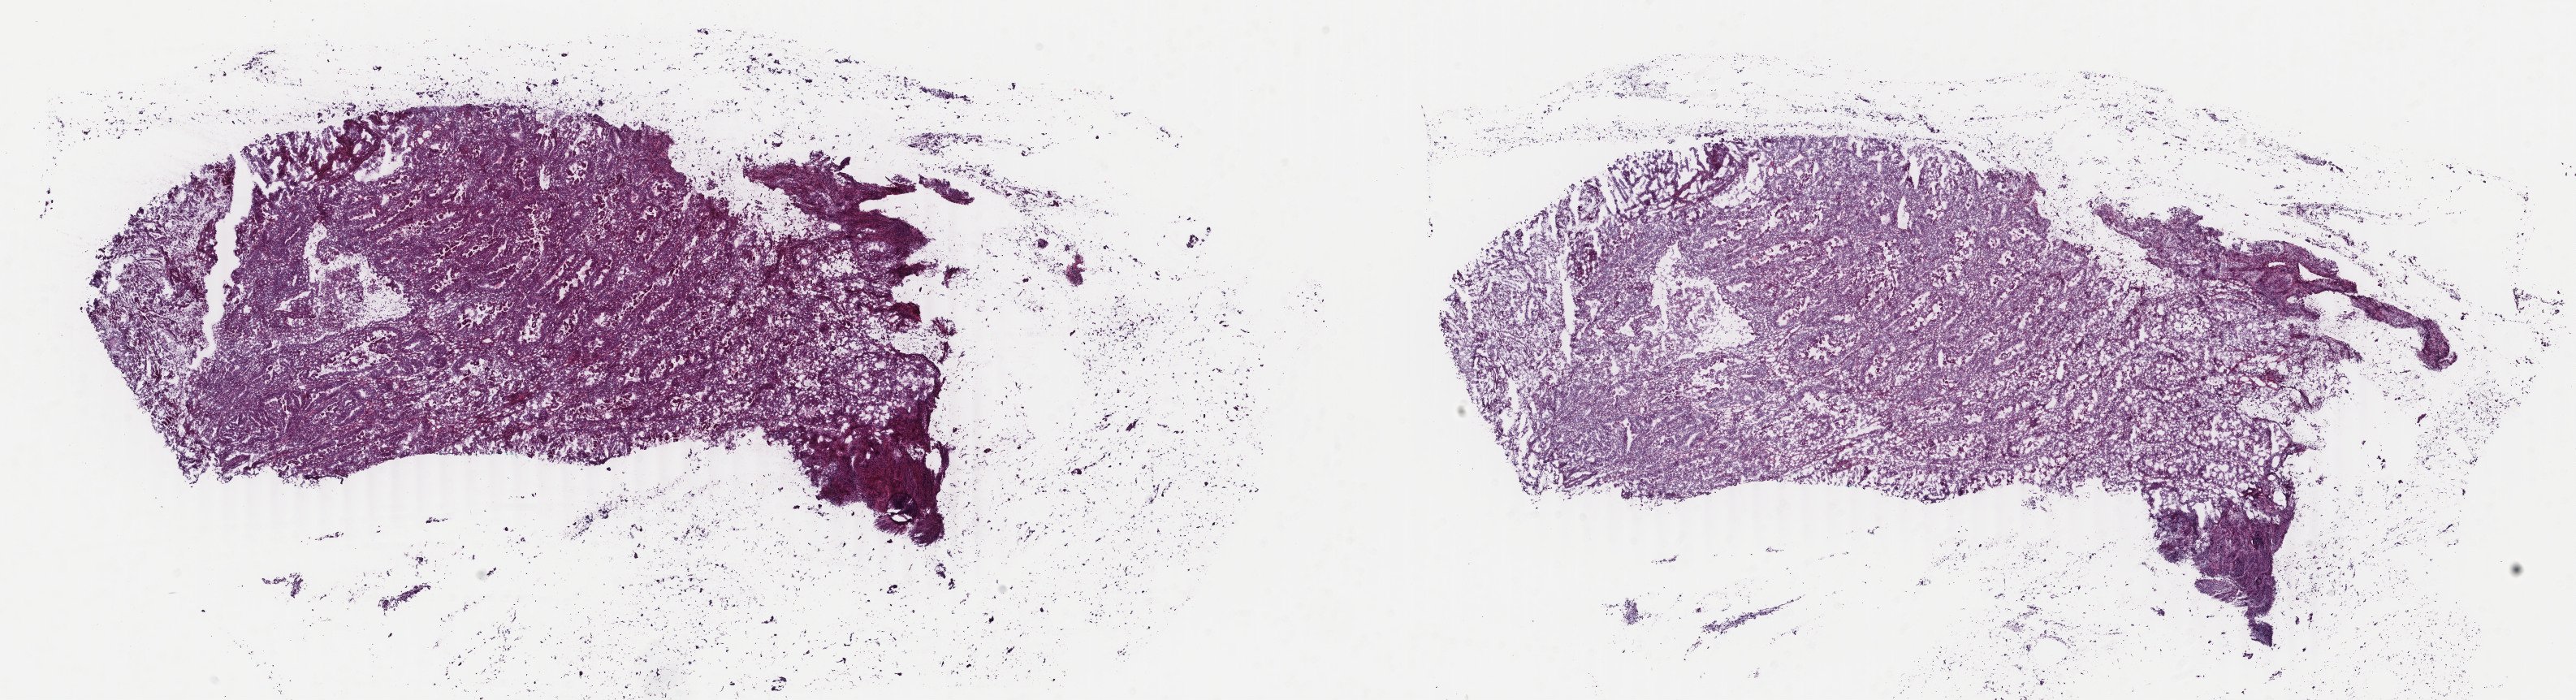
Hematoxylin and eosin (H&E) stained whole-slide image, low-resolution overview of the scanned area, about 25.2 x 6.9 mm (slide scanned at 40x); frozen section; primary tumour sample from the uterus. Female, age 55 years at initial diagnosis. Histologic grade: G1 (well differentiated). Slide review estimates, as recorded: tumour cells 40%, tumour nuclei 30%, normal cells 25%, stromal cells 30%, necrosis 5%. Infiltration values recorded for this section: lymphocyte infiltration 40%, monocyte infiltration 2%, neutrophil infiltration 2%.
FIGO stage: IB. Lymph nodes positive (case pathology): 0 of 8 examined. Diagnosis: Endometrioid adenocarcinoma, NOS (endometrium).